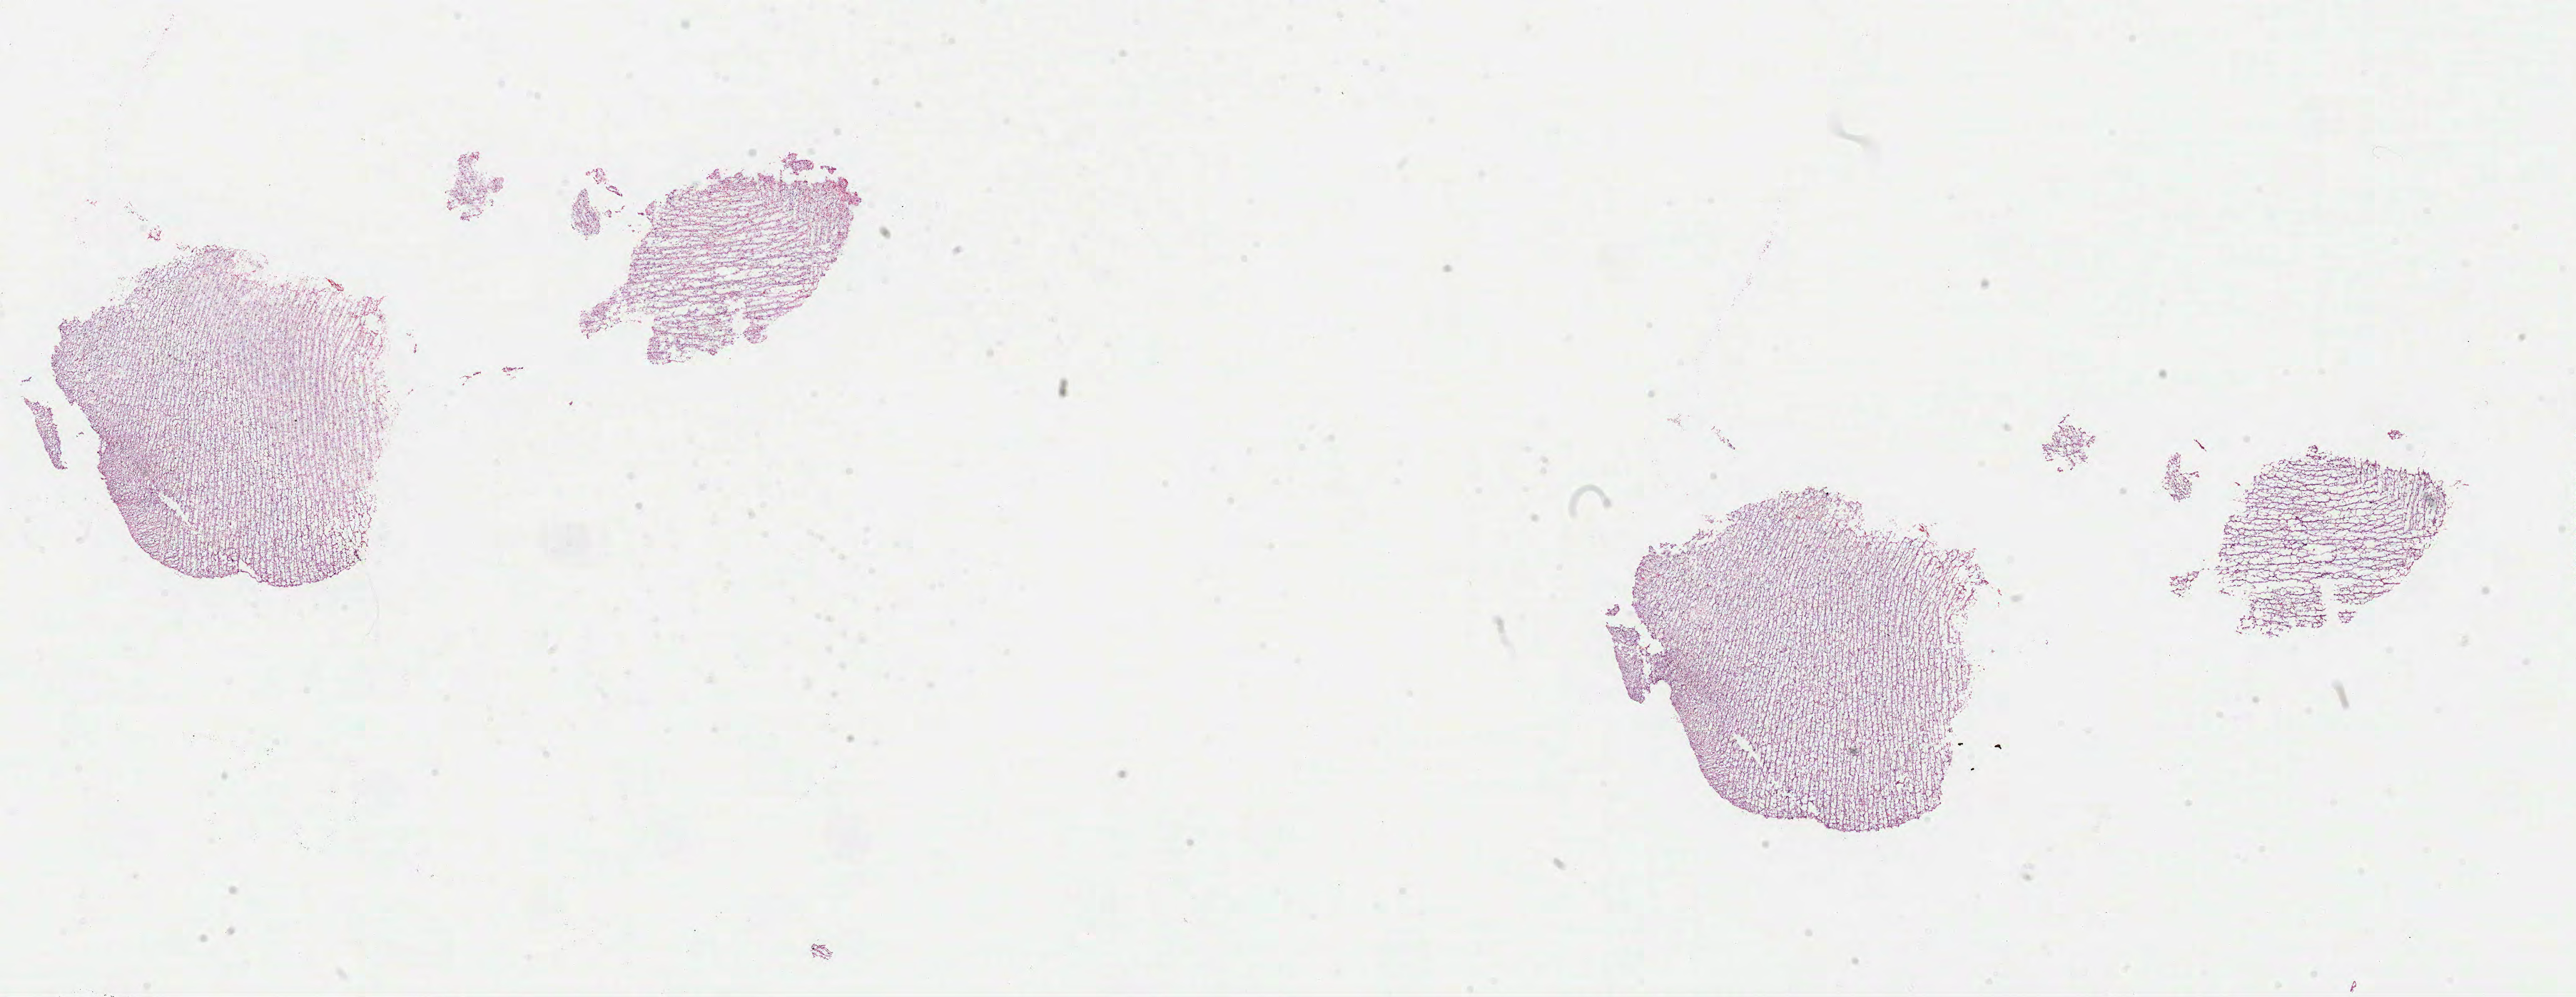
Digitized Hematoxylin and eosin (H&E) stained tissue section (whole slide) — shown as a low-resolution overview of the whole scanned area (about 29.1 x 11.3 mm, from a 40x scan). Frozen section. Brain, primary tumour sample. Female, age 39 years at initial diagnosis. Histologic grade: G2 (moderately differentiated). Slide review estimates, as recorded: tumour cells 100%, tumour nuclei 70%, normal cells 0%, stromal cells 0%, necrosis 0%.
Laterality: right. Diagnosis: Mixed glioma.